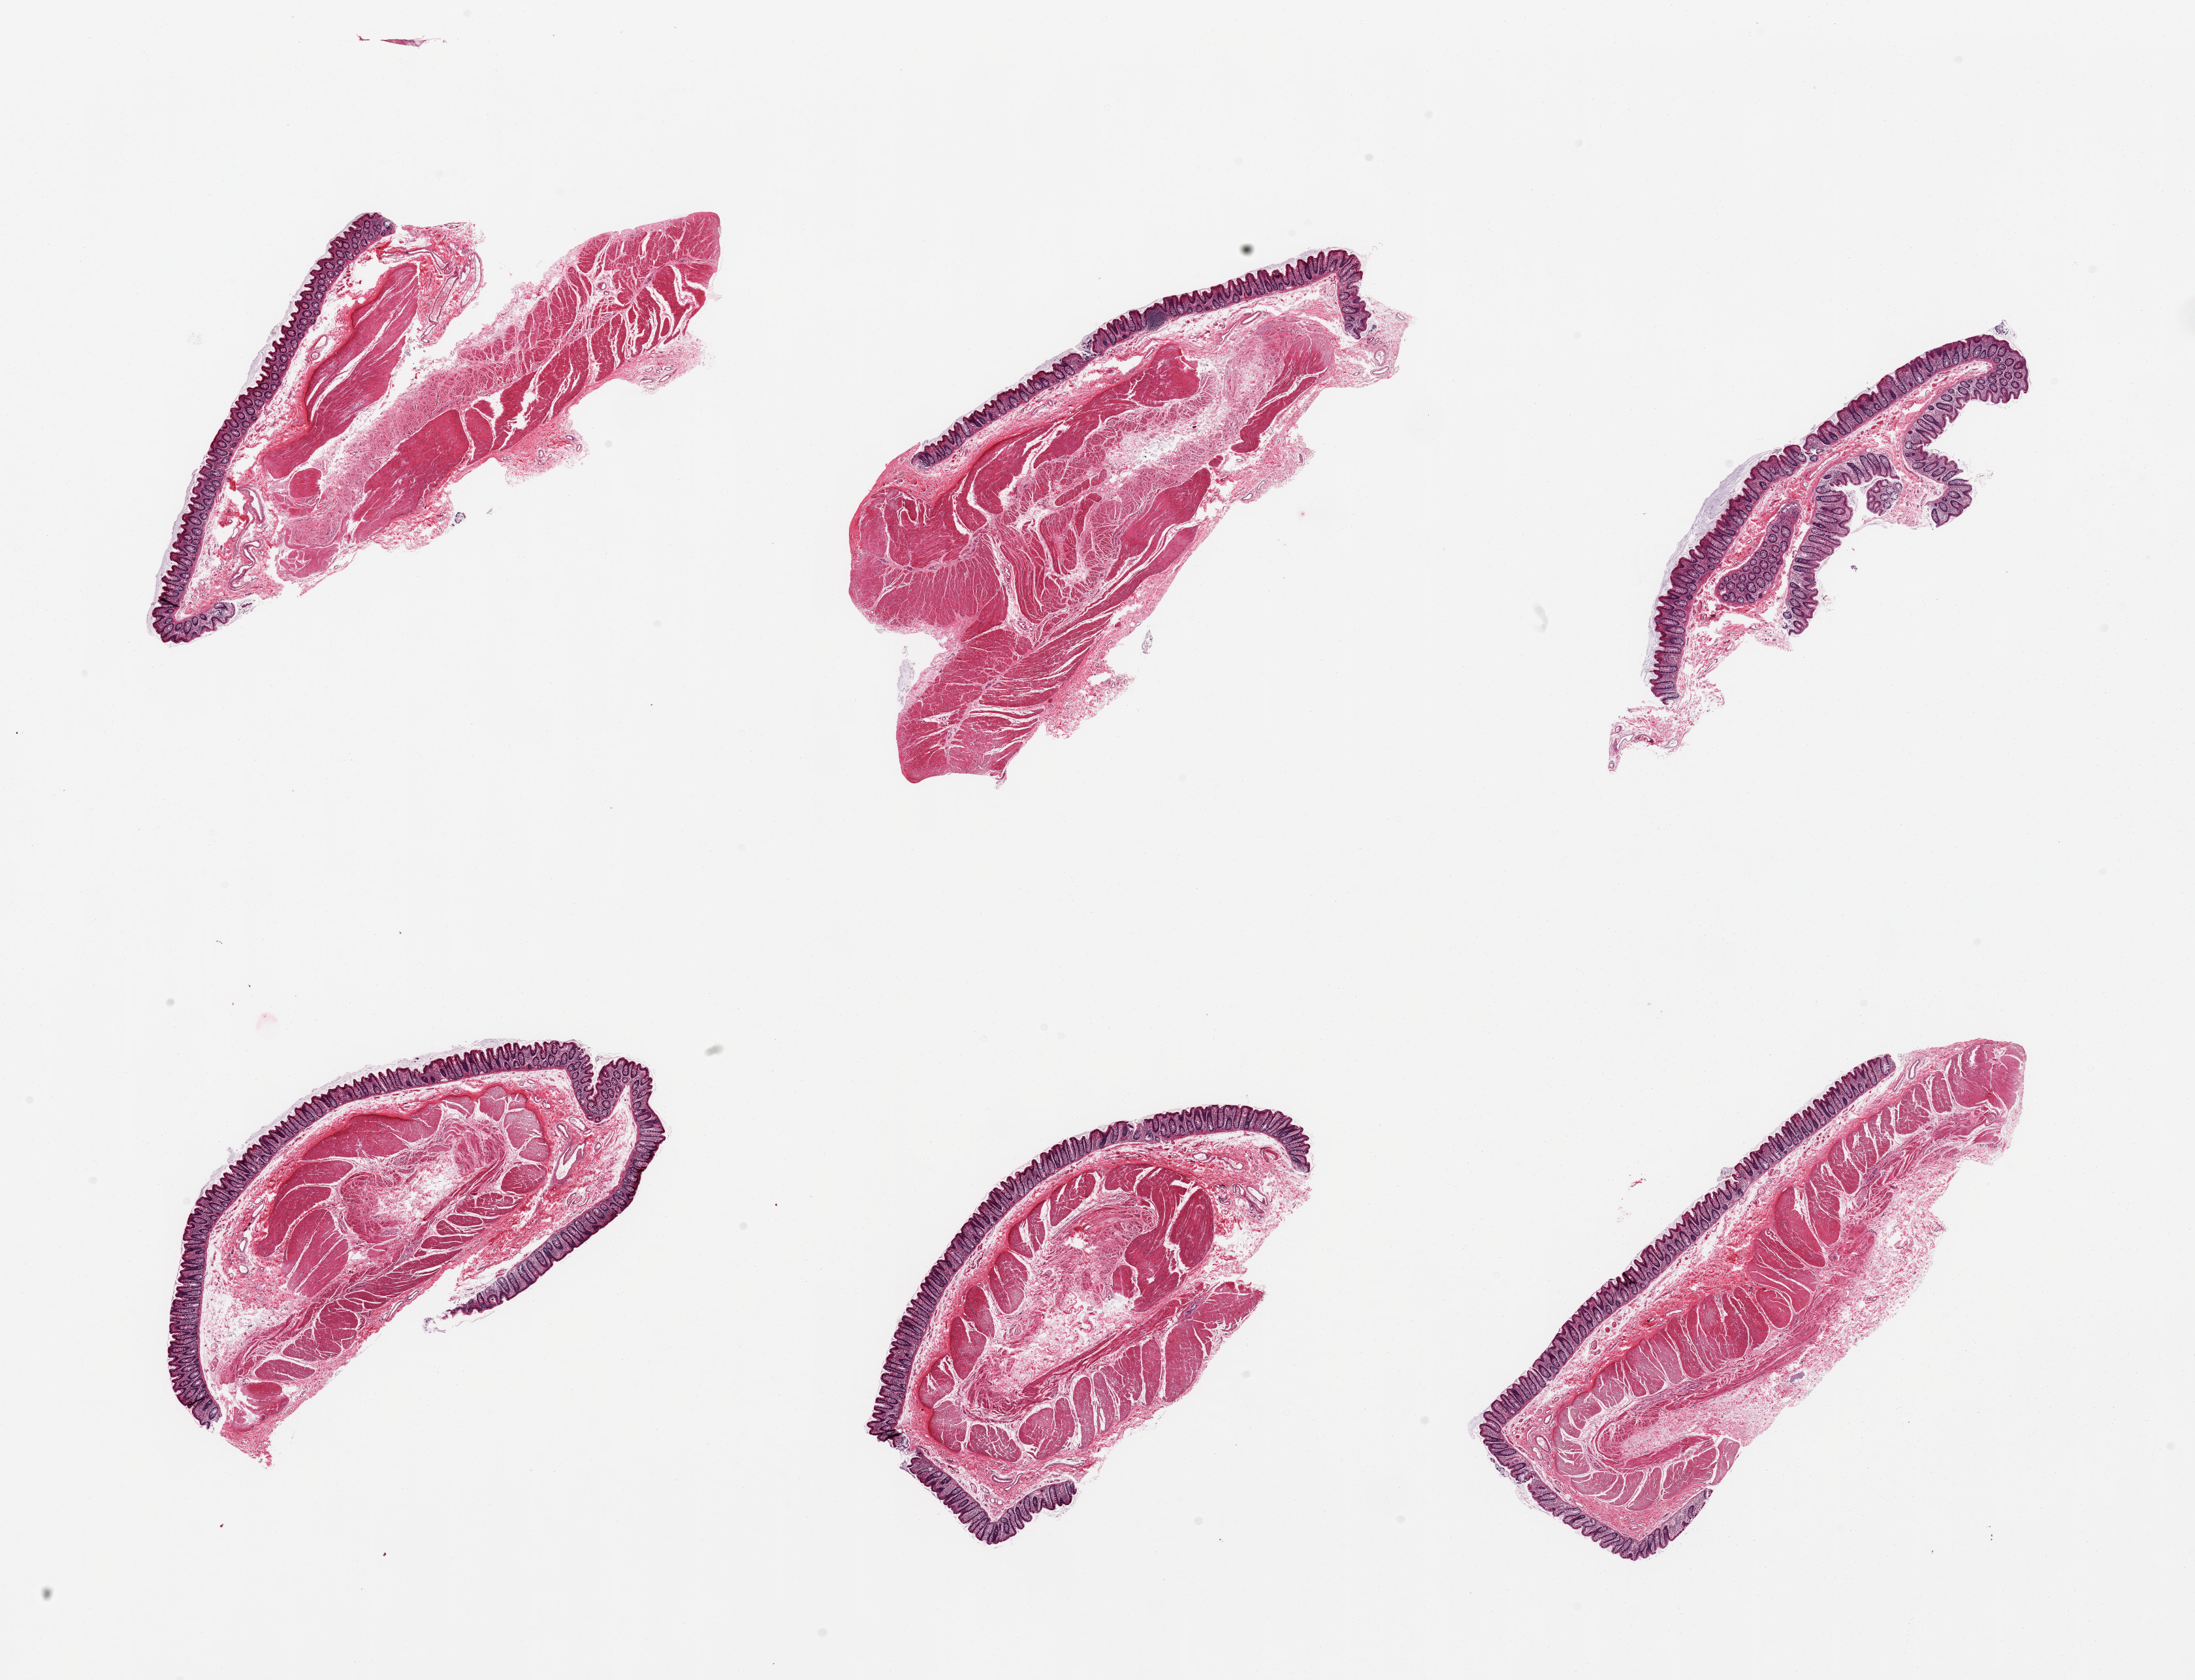
Whole-slide image, hematoxylin and eosin (H&E) stain, whole scanned area (about 26.6 x 20.3 mm) shown as a low-resolution overview. PAXgene-fixed paraffin-embedded (PFPE) section. Target tissue: transverse colon. Tissue donor sample.
- review note (as recorded): 6 pieces; 1 has no muscularis (may represent sampling of 025 aliquot)